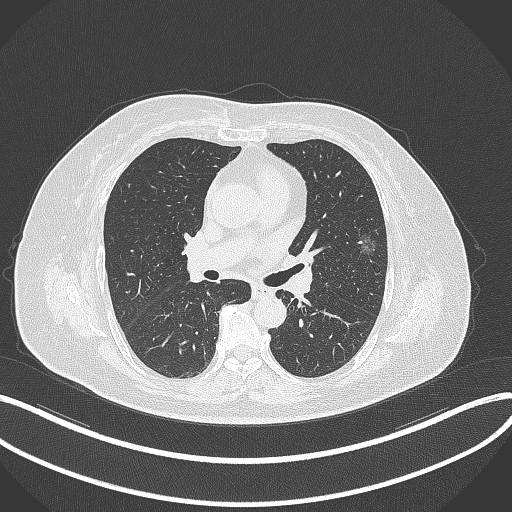
Chest CT, one axial slice. Position 203 of 315 along the scan axis. Reconstruction kernel B70f. Lung window (W 1500 / L -600 HU). 512 × 512 image matrix. Patient: female, 76 years. From the clinical record (not read from this slice): clinical TNM (as recorded): T1b N0 M0; histopathological grade: G1-2.
Outlined on this slice (rectangle marked by the reading radiologist):
- lung tumour (recorded histology: adenocarcinoma): box from (x=353, y=223) to (x=383, y=261) px